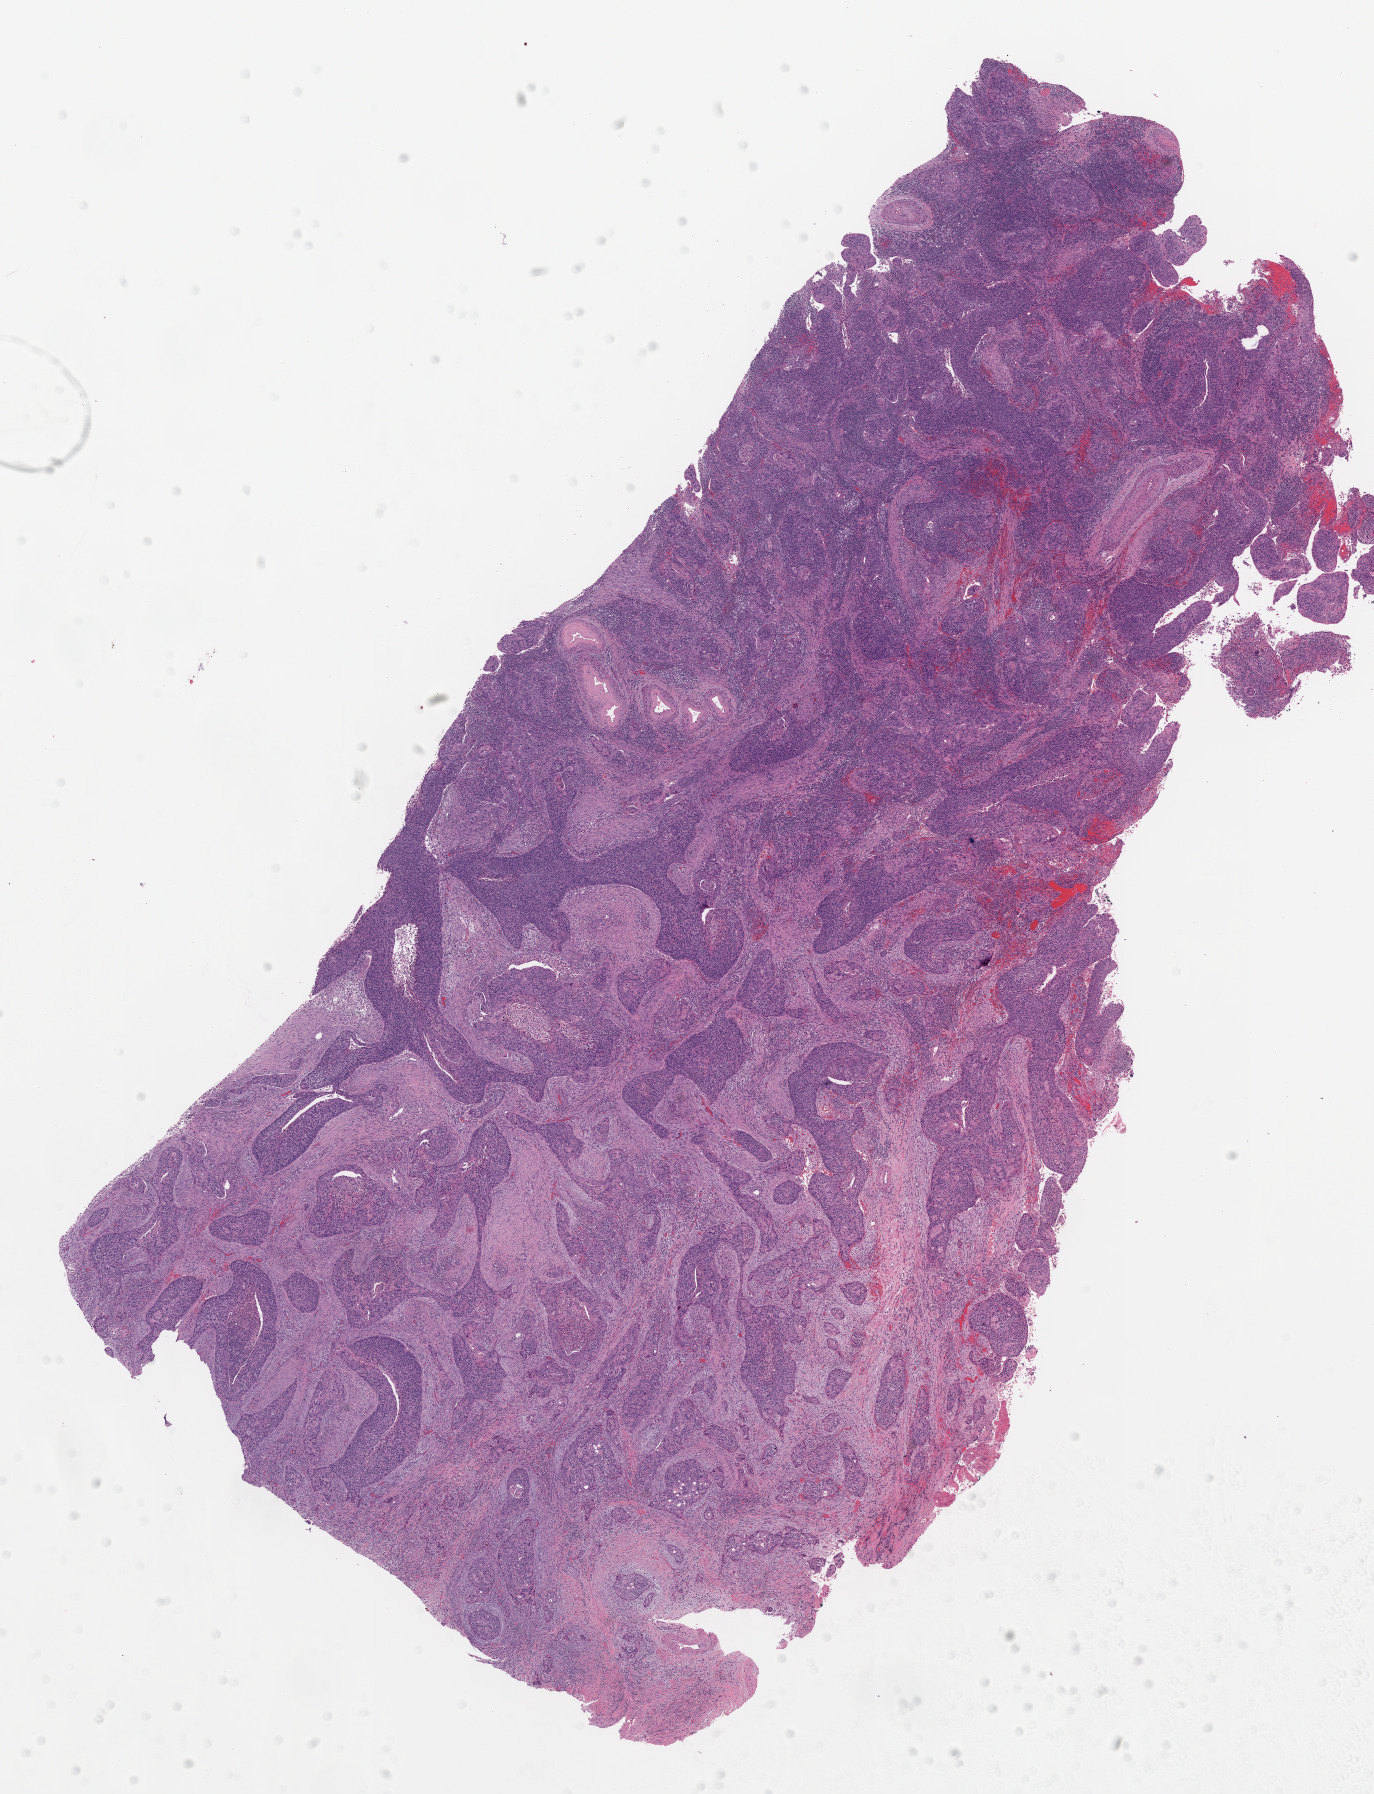
H&E whole-slide image, low-resolution overview of the scanned area, about 11.0 x 14.4 mm, FFPE section, cervix, primary tumour sample. Female, age 53 years at initial diagnosis. Histologic grade: G1 (well differentiated).
Histologic diagnosis: Squamous cell carcinoma, keratinizing, NOS (cervix uteri). FIGO stage: IIA. Lymph nodes positive (case pathology): 0 of 8 examined.